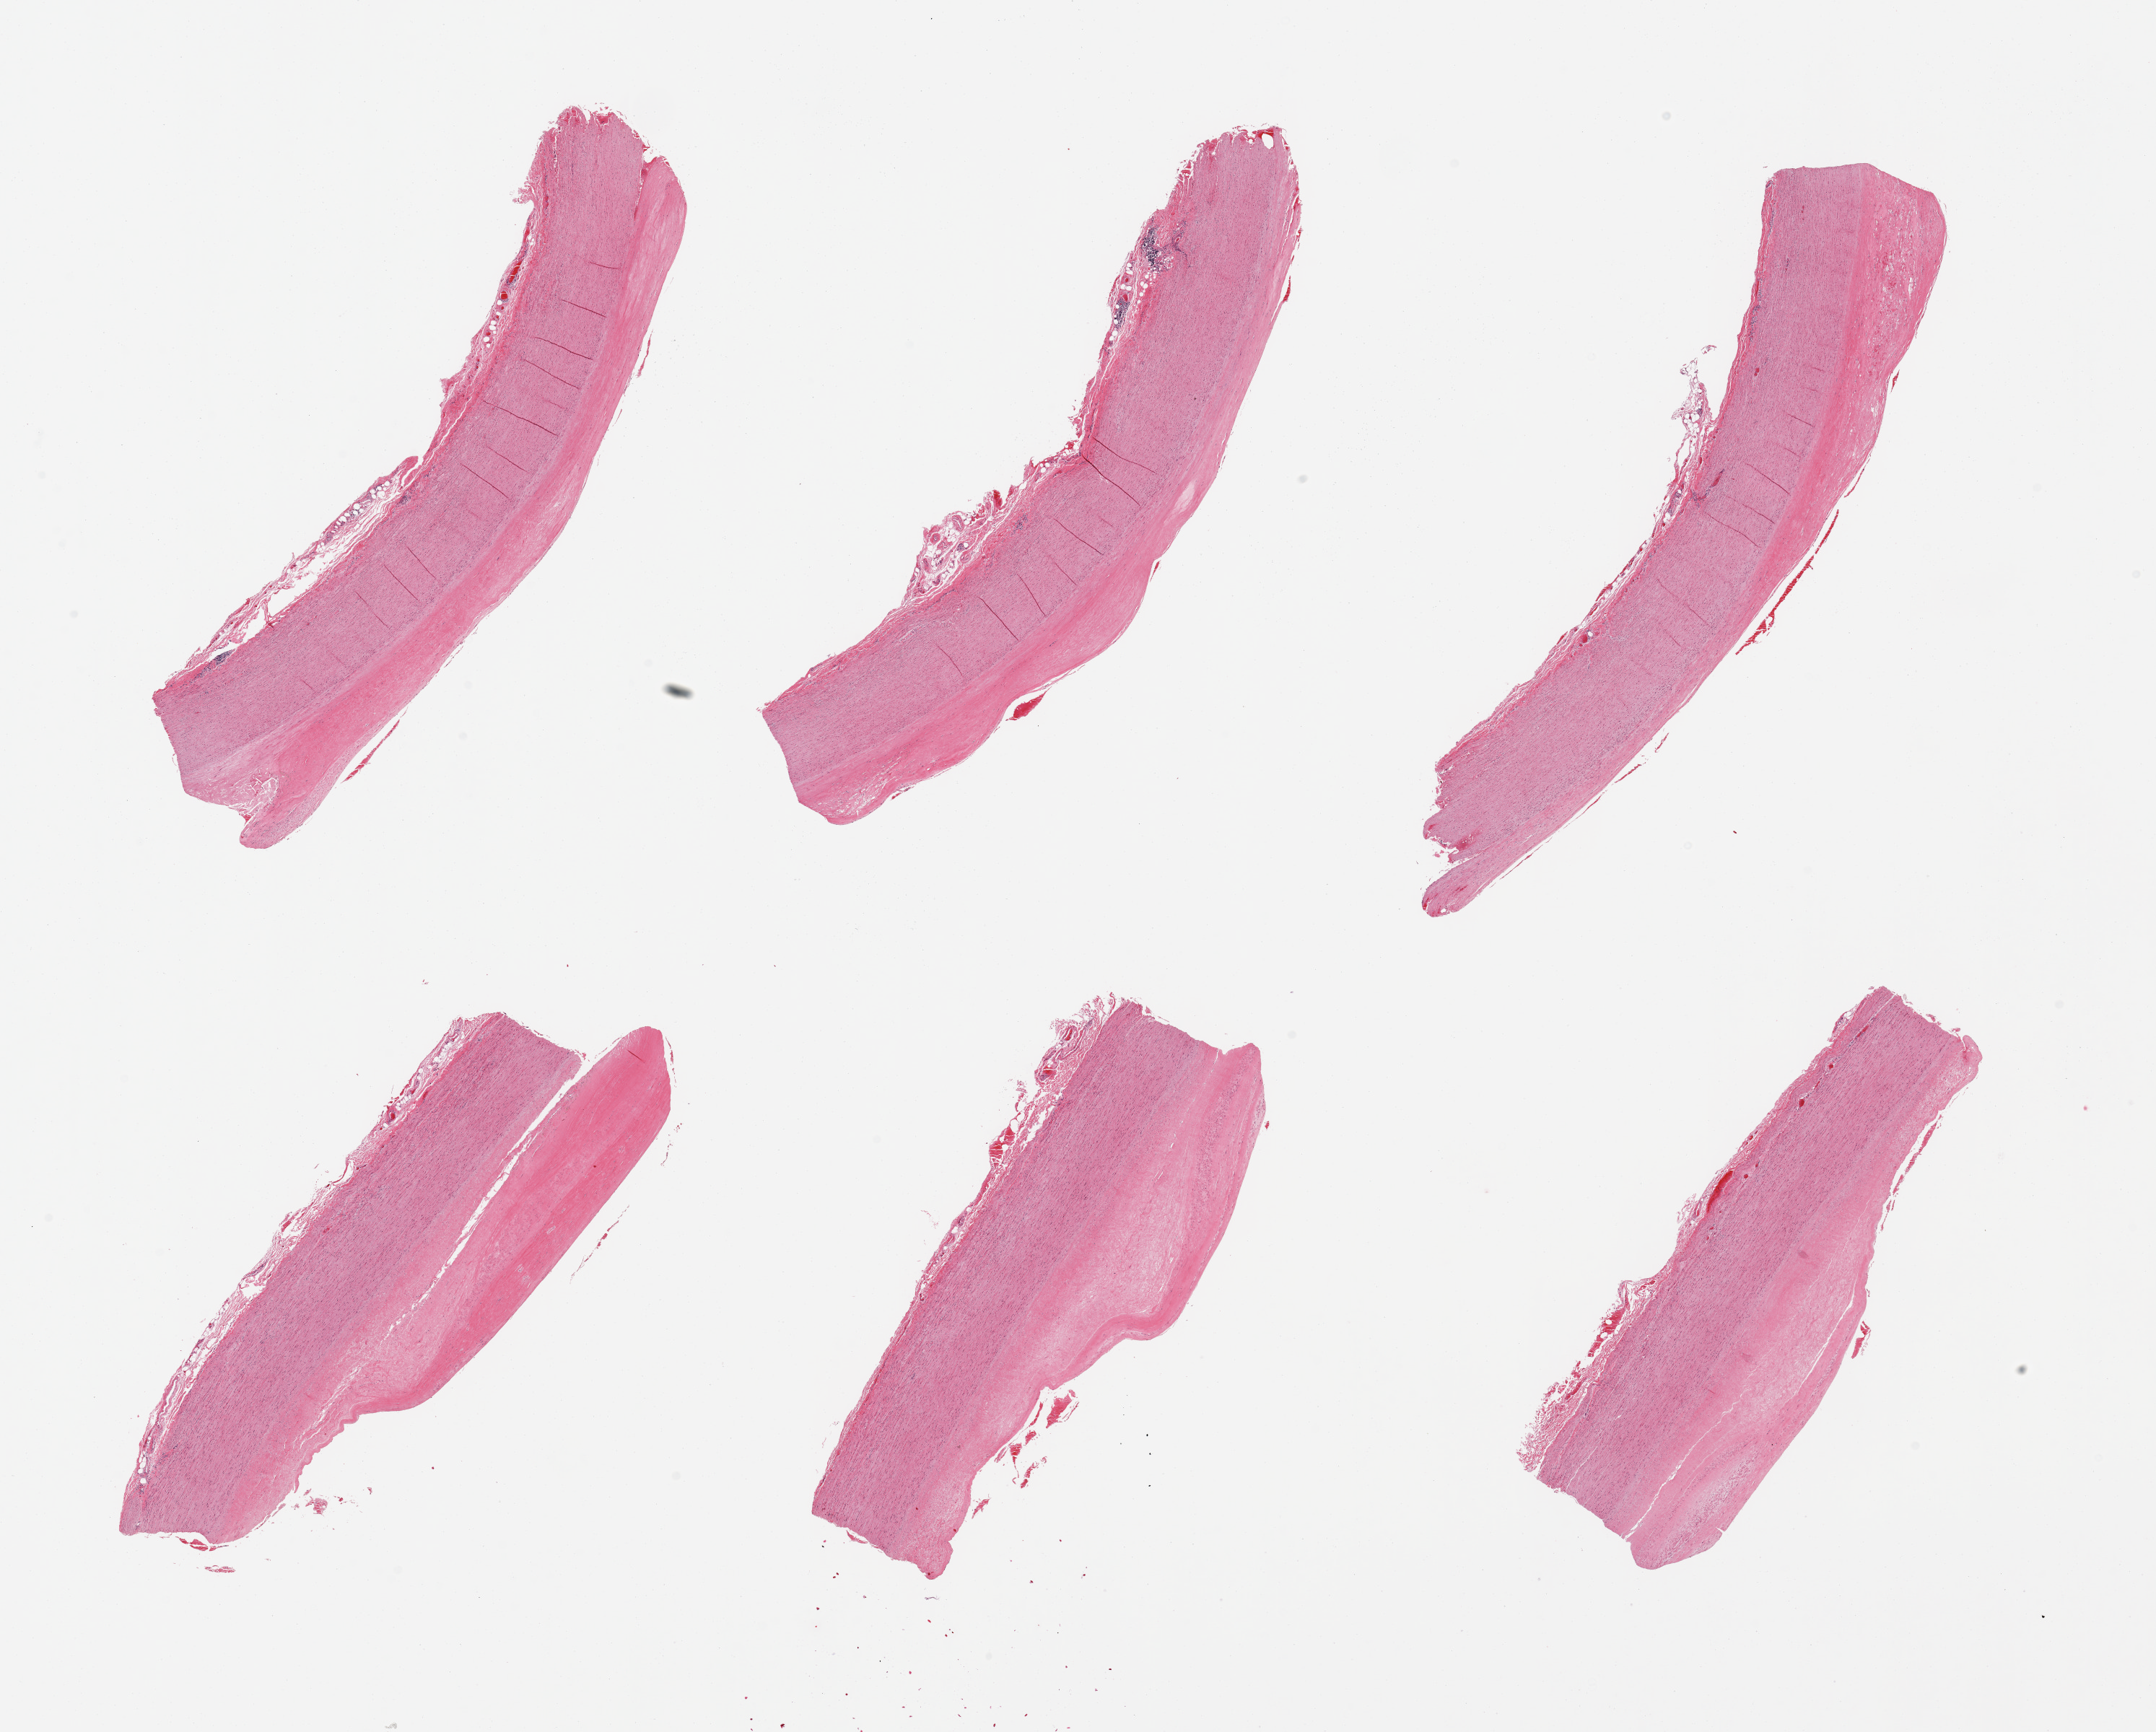
Whole-slide image, H&E stain, brightfield — shown as a low-resolution overview of the whole scanned area (about 23.6 x 19.0 mm); PAXgene-fixed, paraffin-embedded tissue; target tissue: aorta; donor tissue sample. Male donor.
Reviewer comment on this tissue sample: 6 pieces; prominent fibrosclerotic plaques.